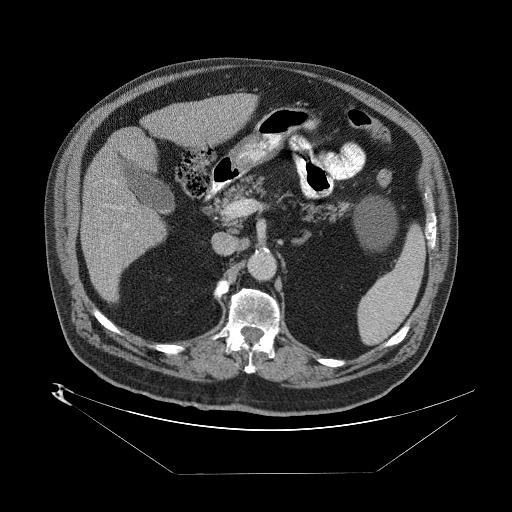
Contrast-enhanced abdominal CT (liver protocol), one axial slice; slice 35 of 89 in the series (ordered by position); reconstruction kernel STANDARD; 140 kVp; one of 2 acquisitions stored at this slice position; soft-tissue window (W 400 / L 40 HU); 2.5 mm slice thickness; 512 × 512 image matrix, field of view 480 × 480 mm. From the clinical record (not read from this slice): diagnosis: hepatocellular carcinoma (patient treated with transarterial chemoembolisation; whether this scan precedes or follows treatment is not stated here); TNM stage (as recorded): Stage-II; Child-Pugh class: B; tumour size: 4 cm.
Structures marked on this image (semi-automatically segmented with operator editing):
- abdominal aorta: bounding box [x1, y1, x2, y2] px = [249, 253, 274, 279]
- liver parenchyma outside the tumour (the mass and vessels are separate outlines, so this box may not span the whole liver): [80, 92, 252, 308]
- liver vessels: [98, 212, 139, 250]